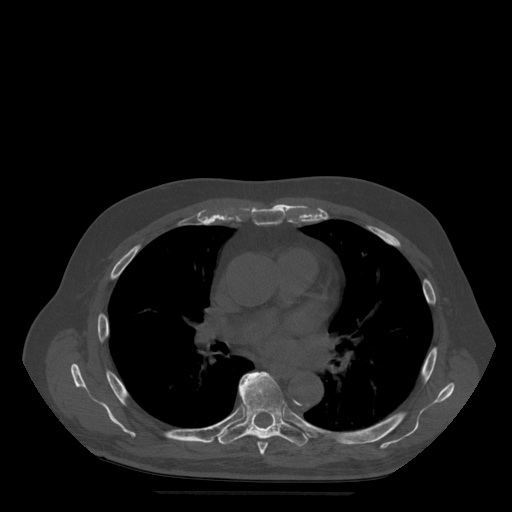
CT including the spine, one axial slice. Slice 339 of 522 in the series (ordered by position). Bone window (W 1800 / L 400 HU). 1.25 mm slice thickness. 512 × 512 image matrix, field of view 420 × 420 mm. Patient age 72 years. Case-level facts recorded for this patient, not image findings: primary cancer: prostate.
Annotated regions visible in this slice (semi-automatic segmentation, software-assisted and operator-edited):
- T6 vertebra: bounding box [x1, y1, x2, y2] px = [240, 372, 270, 456]
- T7 vertebra: [217, 374, 308, 447]